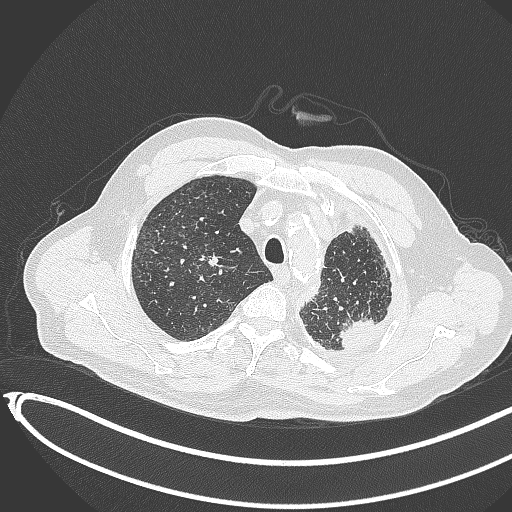
Chest CT, one axial slice; slice 352 of 451 in the series (ordered by position); reconstruction kernel B70f; 120 kVp; lung window (W 1500 / L -600 HU); 512 × 512 image matrix. Male patient, age 78 years. From the clinical record (not read from this slice): clinical TNM (as recorded): T1c N0 M1.
Structures marked on this image (bounding box drawn by a radiologist):
- lung tumour (recorded histology: adenocarcinoma): bounding box (x1, y1, x2, y2) in pixels: (337, 315, 382, 356)